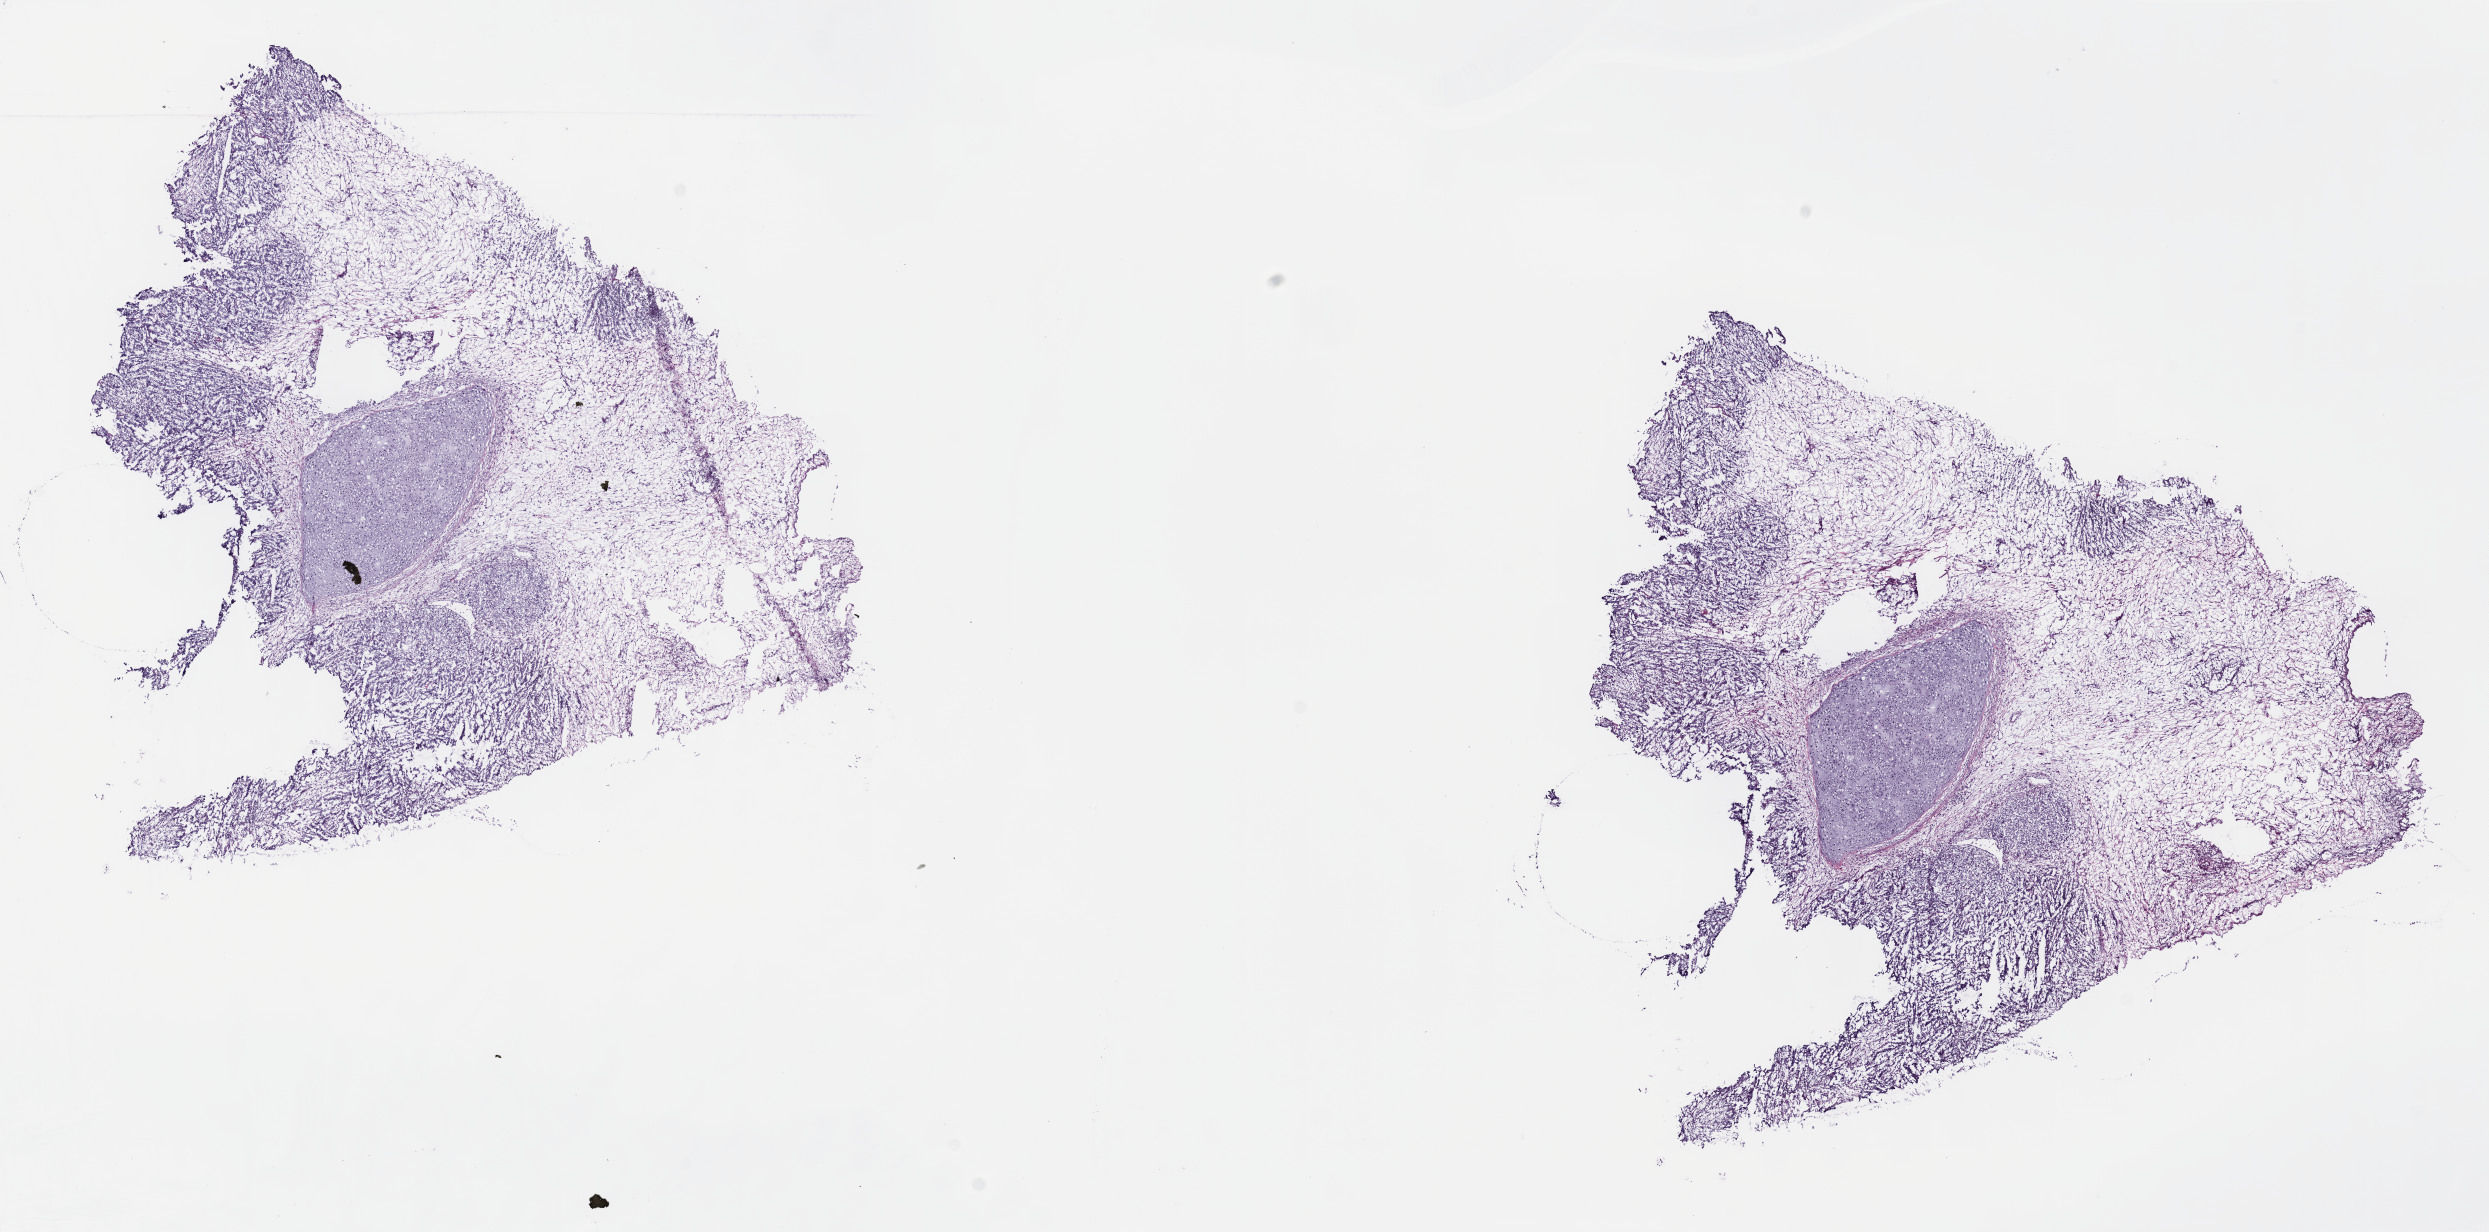
Digitized H&E tissue section (whole slide) — a low-resolution overview of the entire scanned area, about 20.1 x 10.0 mm (slide scanned at 40x); frozen section; primary tumour sample from the testis. Male patient; age at initial diagnosis 33 years. Composition of this section per pathologist review: tumour cells 75%, tumour nuclei 75%, normal cells 0%, stromal cells 25%, necrosis 0%. Infiltration values recorded for this section: lymphocyte infiltration 4%, monocyte infiltration 1%, neutrophil infiltration 2%.
• laterality: left
• TNM: T1 N0 M0
• AJCC pathologic stage: IS
• pathologic diagnosis: Mixed germ cell tumor